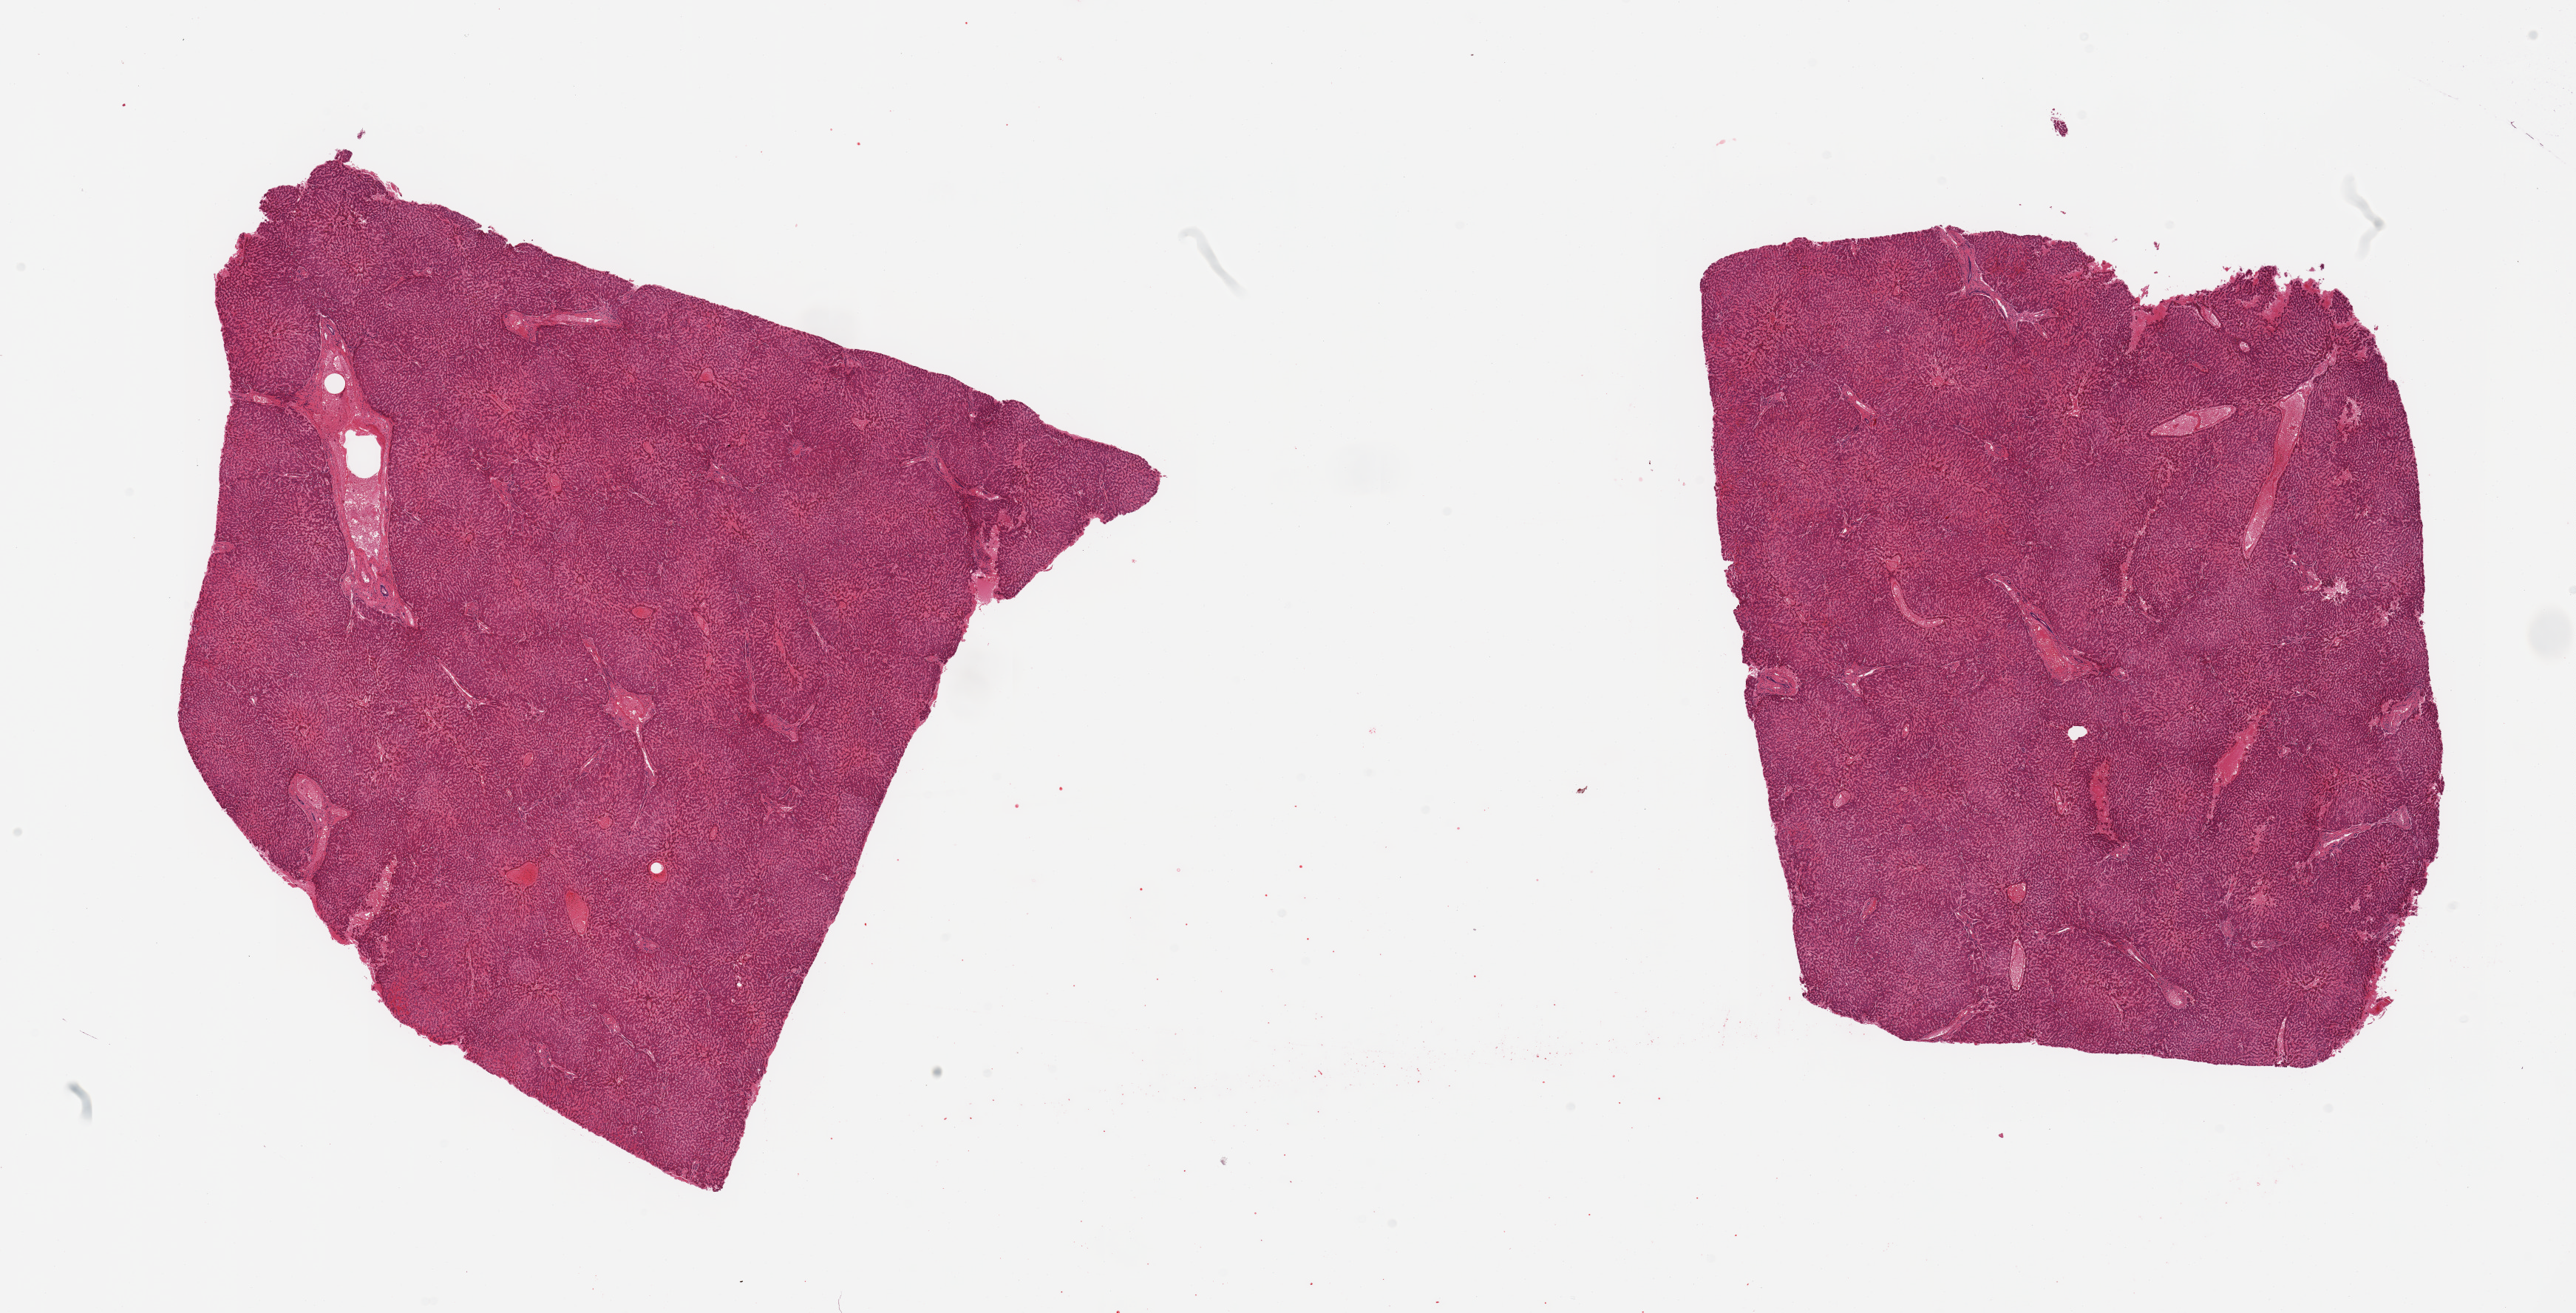
Whole-slide image, H&E stain — low-resolution overview of the scanned area, about 27.6 x 14.0 mm. PAXgene-fixed paraffin-embedded (PFPE) section. Section of liver (target tissue). Donor tissue sample. Donor sex: male.
Reviewer comment on this tissue sample: 2 pieces; moderate central vein congestion.